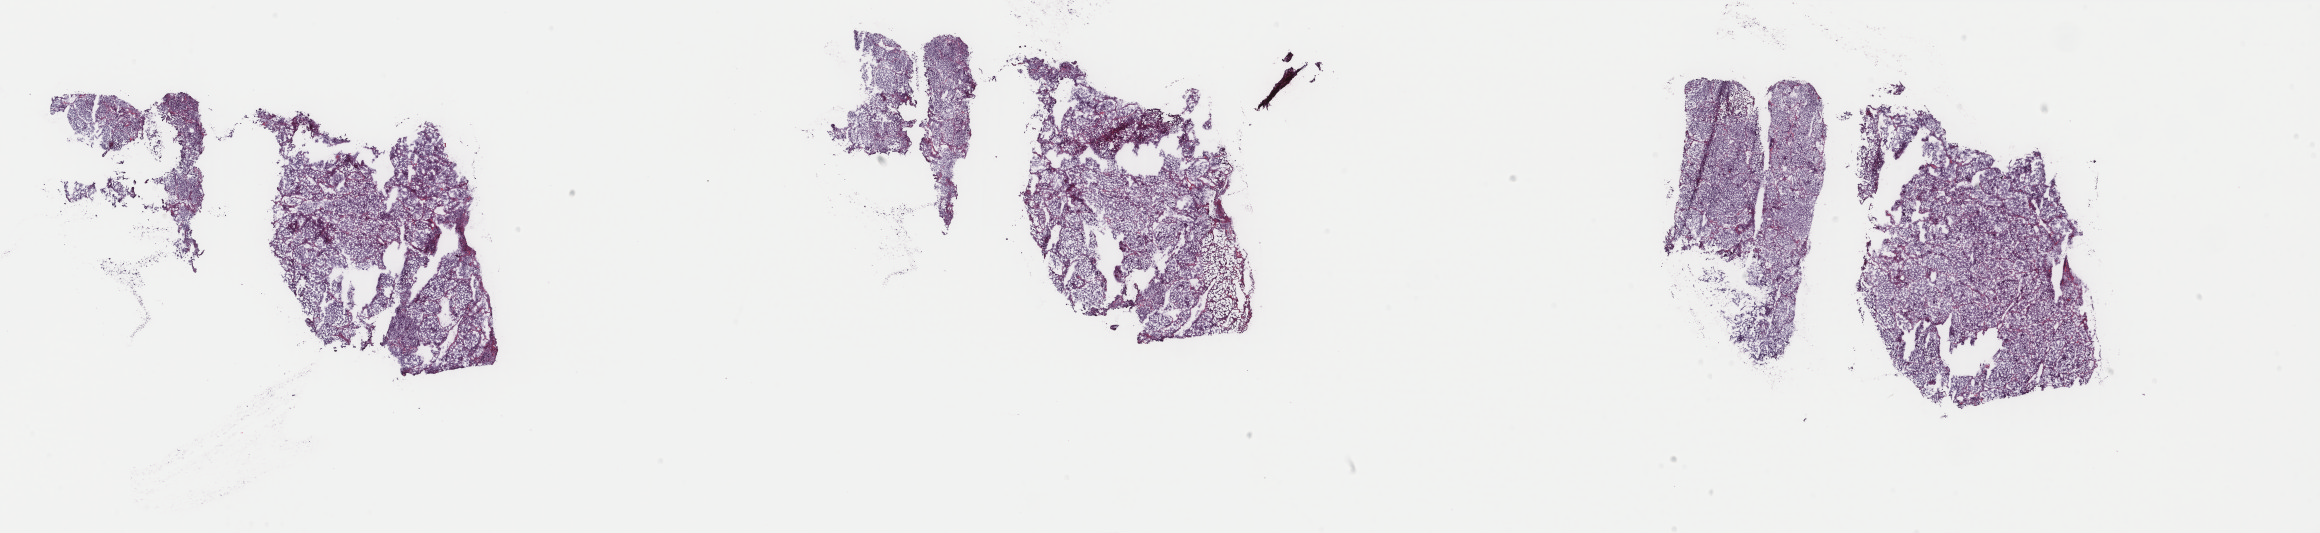
Digitized Hematoxylin and eosin (H&E) stained tissue section (whole slide), low-resolution overview of the scanned area, about 36.8 x 8.5 mm (slide scanned at 40x). Frozen section from the top of the tissue portion. Adrenal gland, primary tumour sample. Female patient; age at initial diagnosis 28 years. Composition of this section per pathologist review: tumour cells 90%, tumour nuclei 95%, normal cells 0%, stromal cells 10%, necrosis 0%. Infiltration values recorded for this section: lymphocyte infiltration 0%, monocyte infiltration 0%, neutrophil infiltration 0%.
Histologic diagnosis: Pheochromocytoma, NOS.